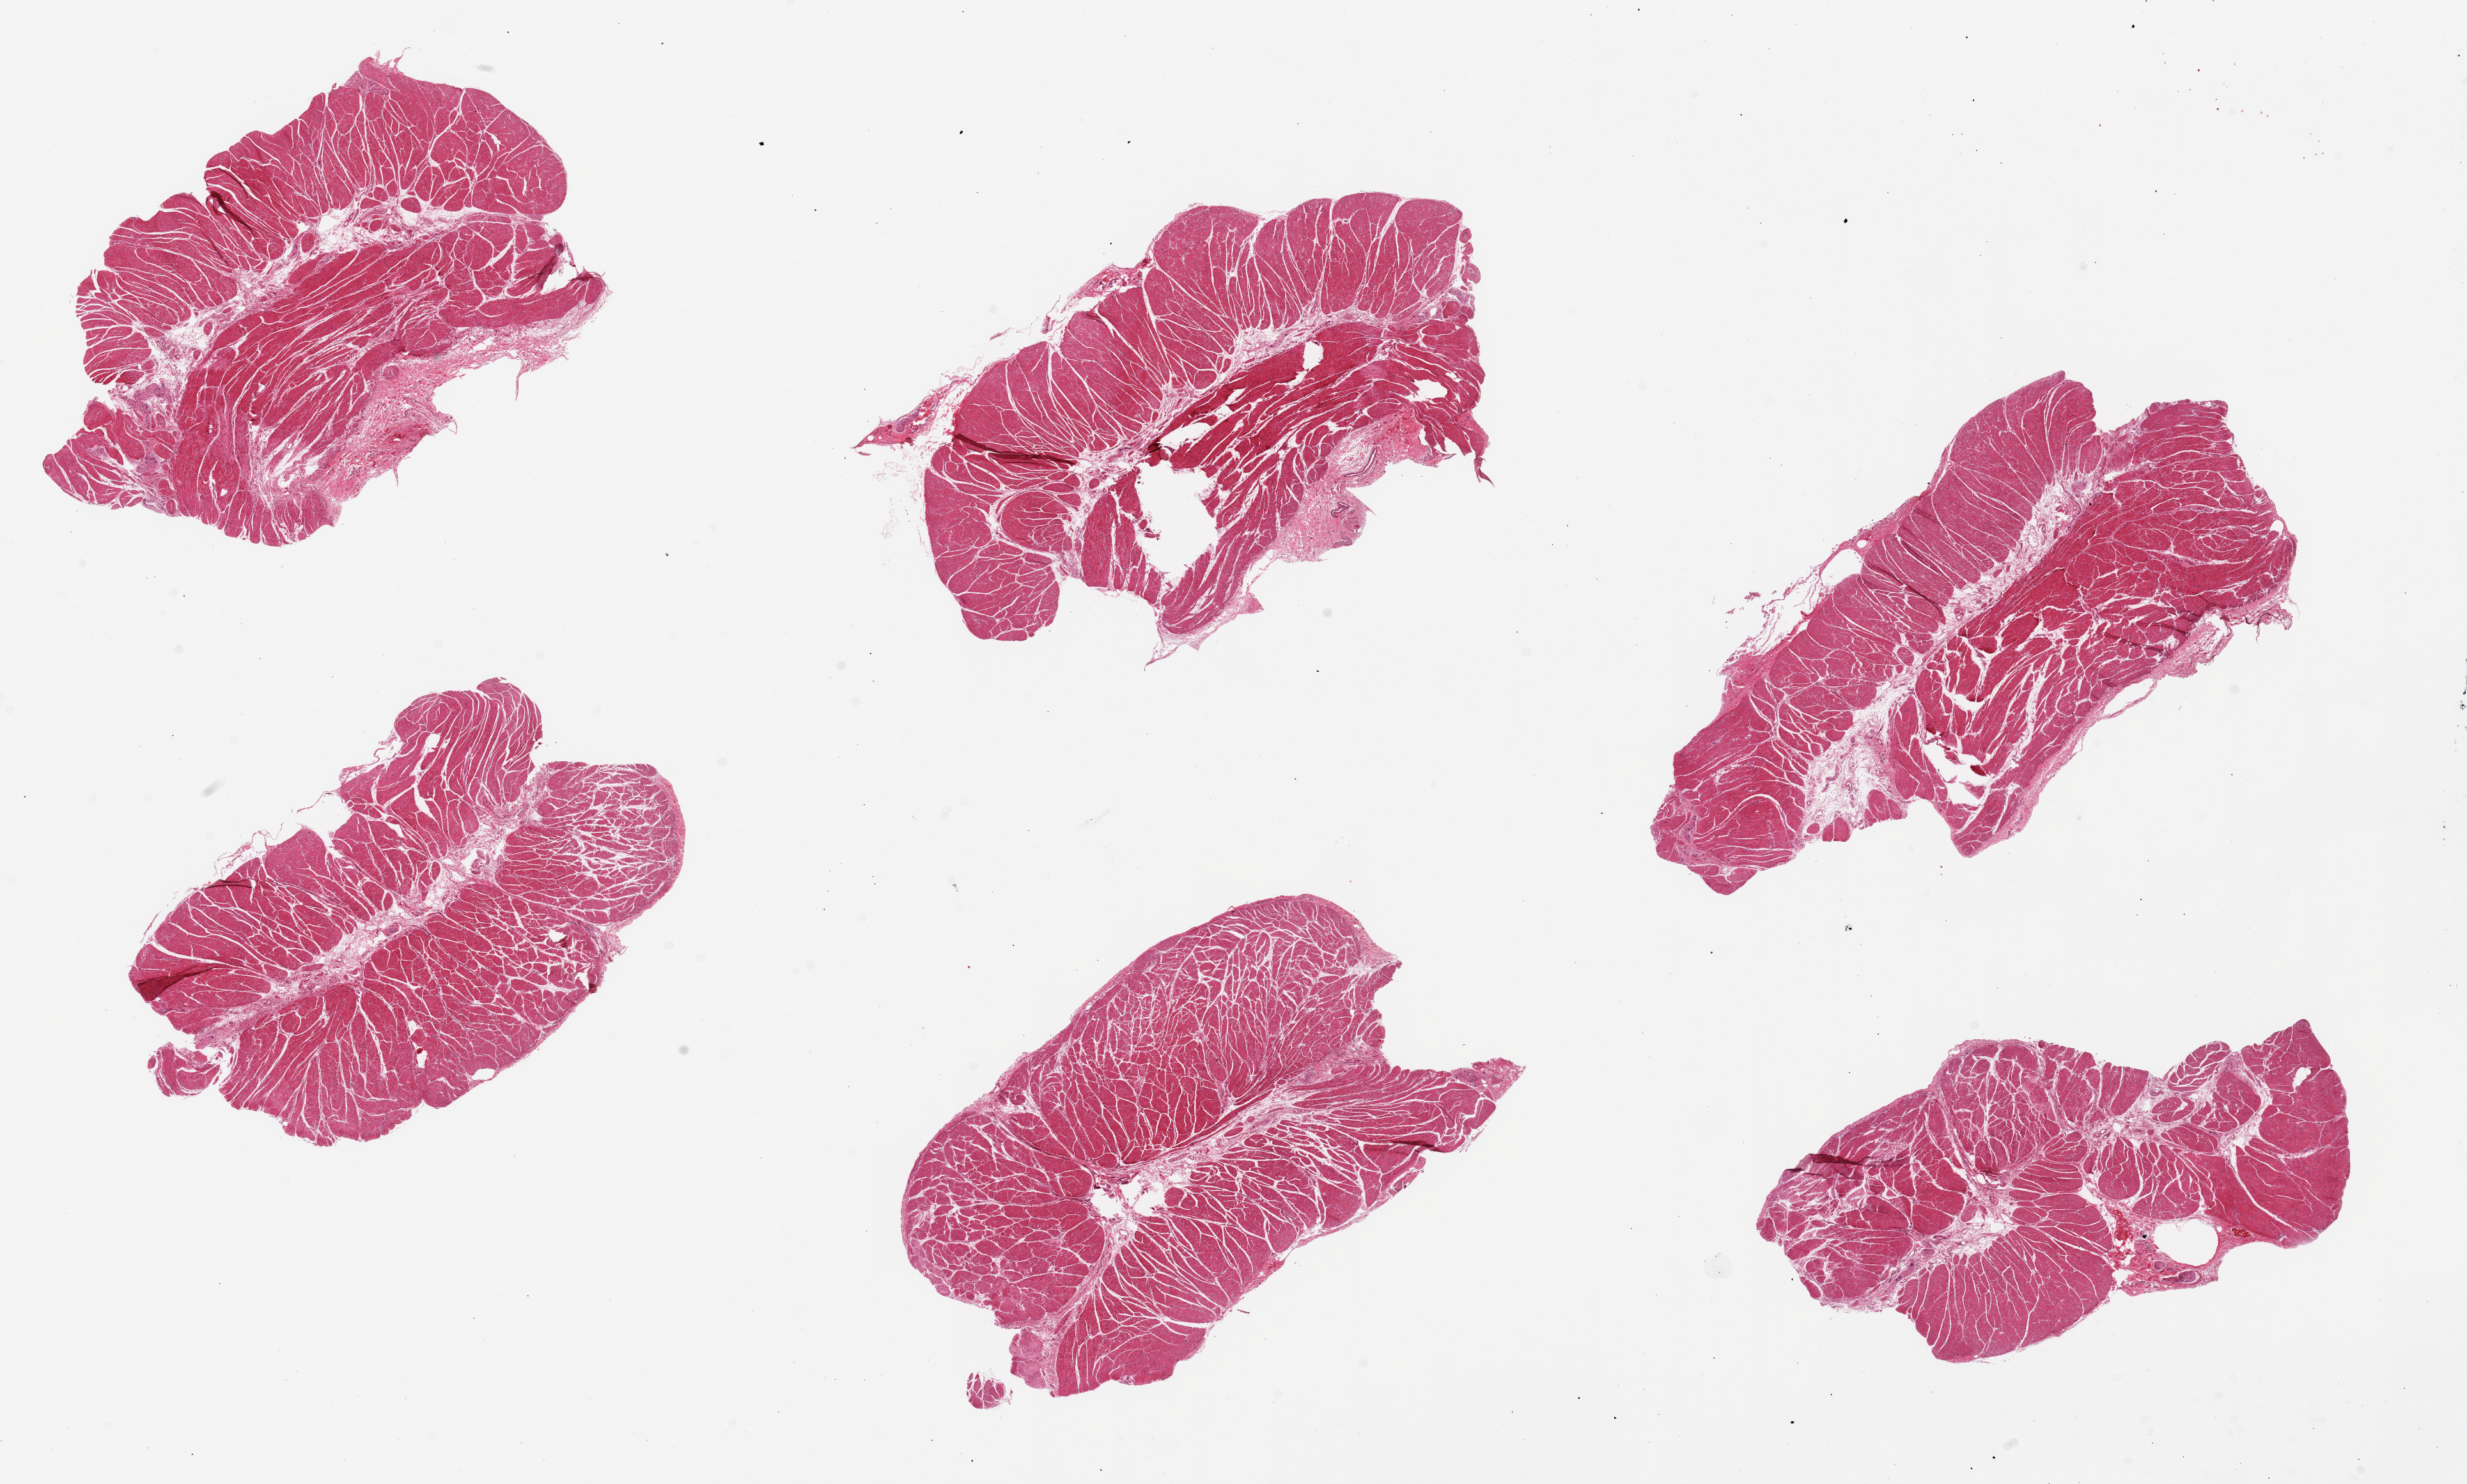
Whole-slide image, hematoxylin and eosin (H&E) stain, low-resolution overview of the scanned area, about 30.5 x 18.4 mm. PAXgene-fixed, paraffin-embedded tissue. Sampled site (target tissue): esophageal muscle. Donor tissue sample.
Pathologist's review note for this sample: 6 pieces, up to 9x4.5mm; all muscularis, good specimens.